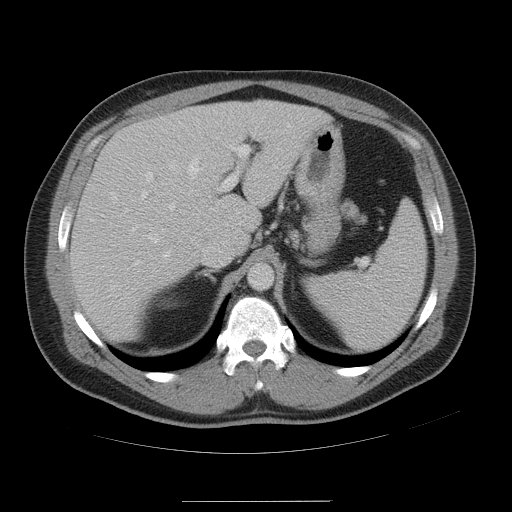
Contrast-enhanced abdominal CT, one axial slice. Slice 35 of 54 in the series (ordered by position). 120 kVp. Intravenous contrast given. Soft-tissue window (W 400 / L 40 HU). 5 mm slice thickness. 512 × 512 image matrix. Male patient, age 40 years. Case-level facts recorded for this patient, not image findings: diagnosis: colorectal cancer liver metastases, imaged before liver resection; multiple liver metastases: no; largest metastasis: 15 cm; disease in both lobes: no.
Outlined on this slice (expert manual segmentation):
- hepatic veins: box from (x=148, y=157) to (x=201, y=257) px
- liver: (x=70, y=100)–(x=331, y=343)
- planned liver remnant (the part of the liver to remain after resection): (x=188, y=100)–(x=331, y=265)
- portal vein (with intrahepatic branches): (x=142, y=135)–(x=250, y=211)